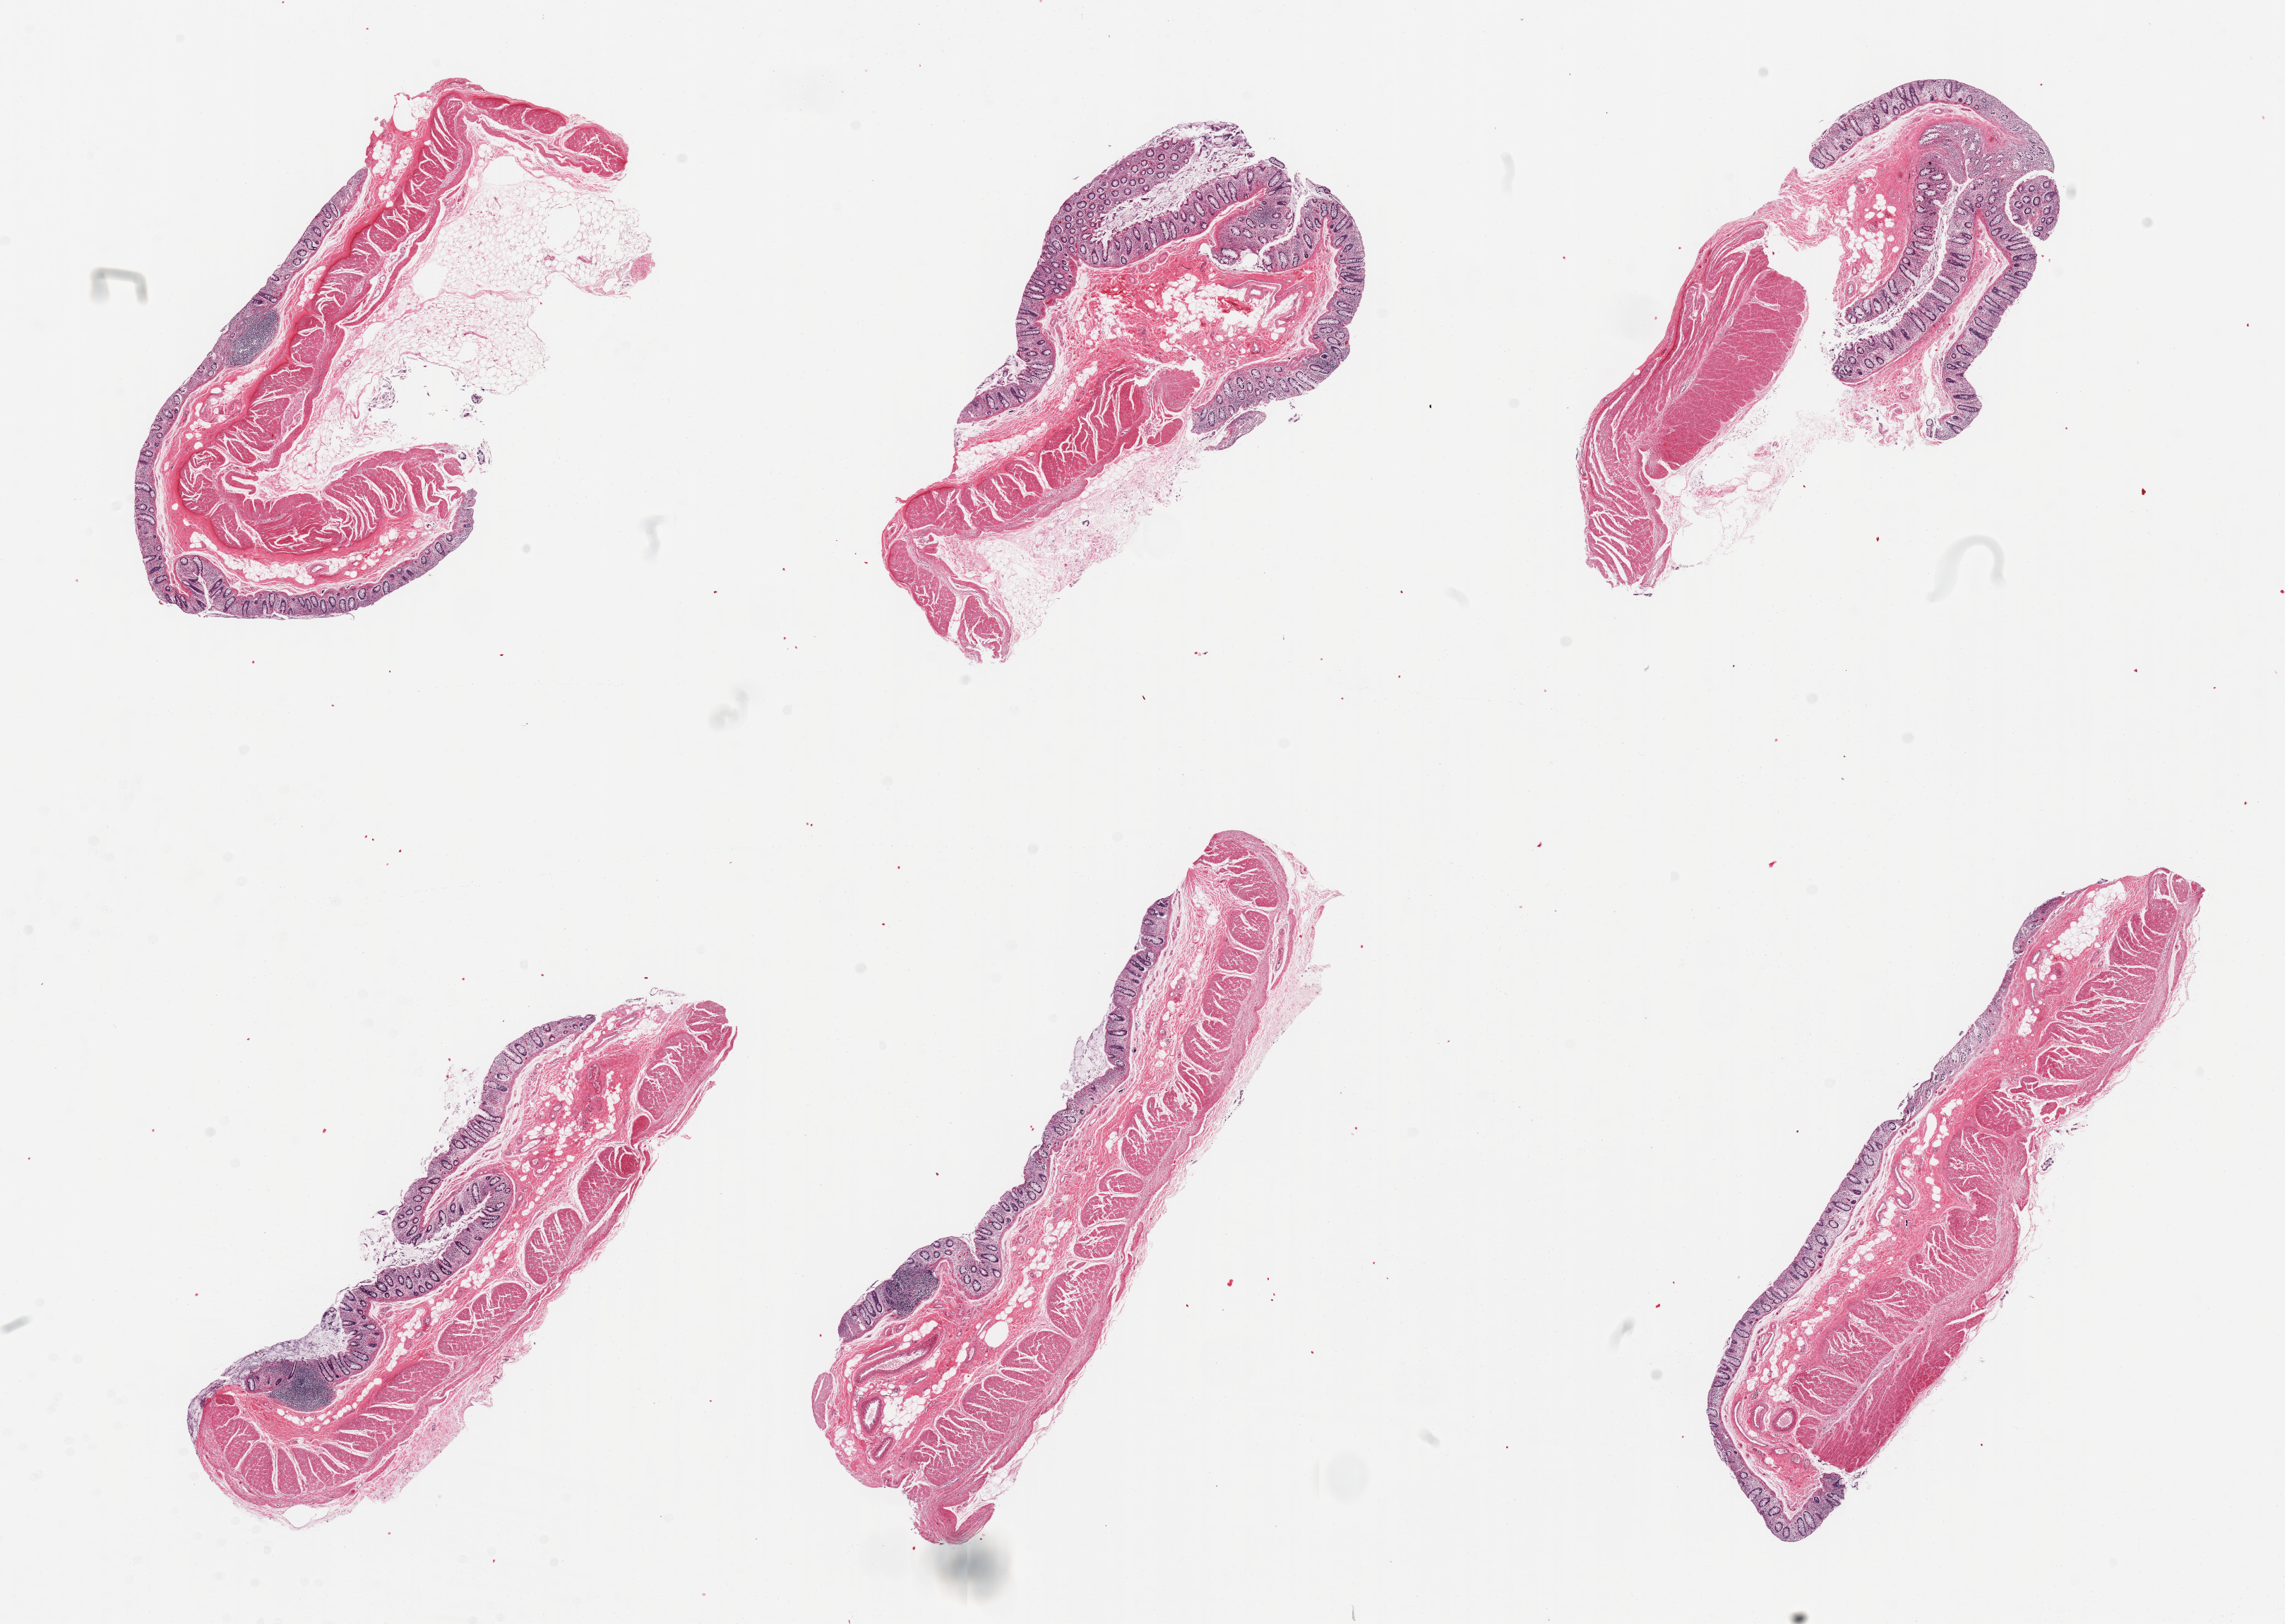
Whole-slide image, H&E stain — low-resolution overview of the scanned area, about 25.6 x 18.2 mm (slide scanned at 20x). PAXgene-fixed, paraffin-embedded tissue. Sampled site (target tissue): transverse colon. Tissue donor sample. Male donor.
Pathologist's review note for this sample: 6 pieces, partially autolyzed mucosa (predominantly 2, some autolysis 3) and muscularis.